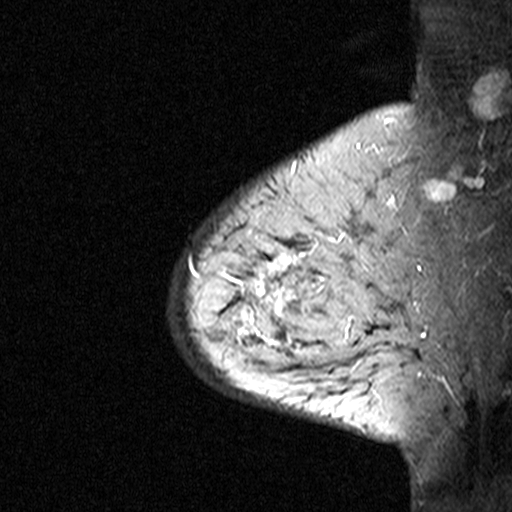
Breast MRI (dynamic contrast-enhanced), one sagittal slice; slice 34 of 44 in the series (ordered by position); dynamic contrast-enhanced study with each time point stored as its own series, time point 3 of 4 at this slice position (ordered by acquisition time); 1.5 T; TE 4.5 ms, TR 11 ms; 3 mm slice thickness; 512 × 512 image matrix. Female patient, age 65 years. From the clinical record (not read from this slice): setting: breast cancer imaged before/during neoadjuvant chemotherapy; receptor status: HER2-positive.
Structures marked on this image (semi-automatic segmentation, software-assisted and operator-edited):
- analysis volume of interest (the breast-tissue region the enhancement analysis was run in; not a lesion): bounding box (x1, y1, x2, y2) in pixels: (182, 190, 353, 361)
- tumour enhancement mask (voxels above the 90 % enhancement threshold inside the analysis volume of interest): (189, 249, 306, 348)